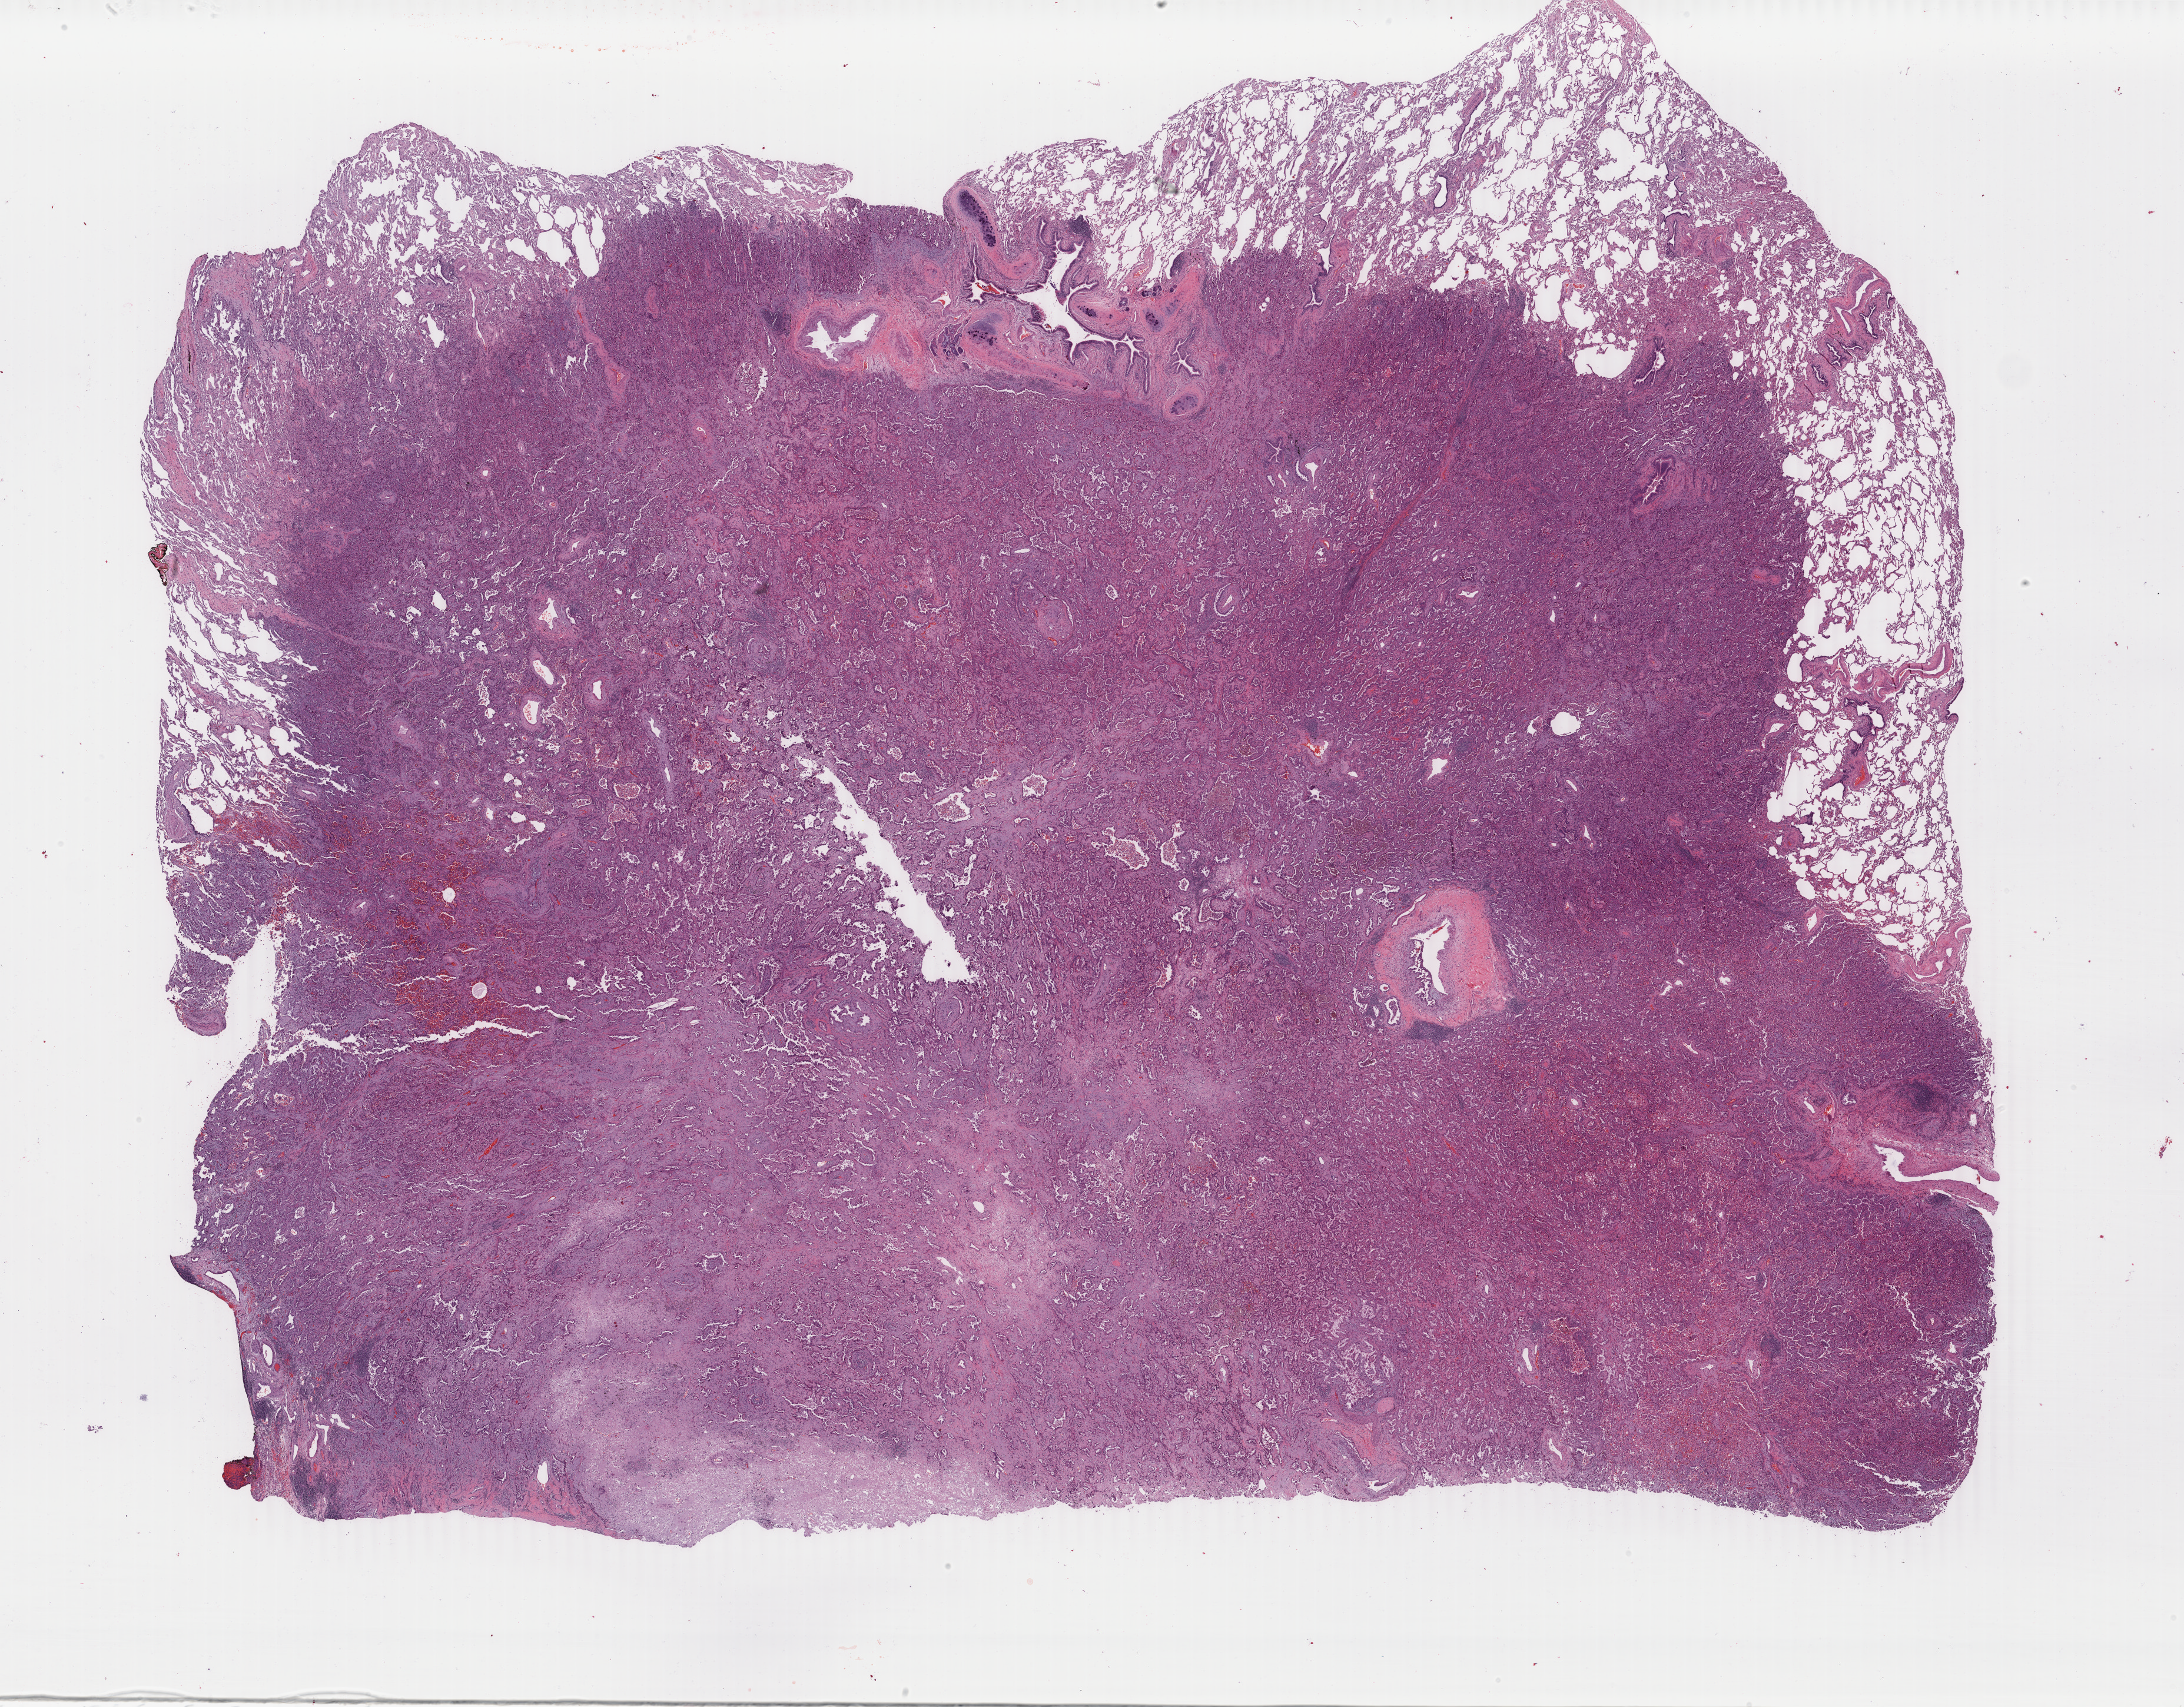
H&E whole-slide image, a low-resolution overview of the entire scanned area, about 29.5 x 23.1 mm, FFPE section, sample: primary tumour, lung. Patient: female, age at initial diagnosis 59 years.
AJCC pathologic stage: IB (7th edition). Histologic diagnosis: Adenocarcinoma with mixed subtypes (lower lobe, lung).